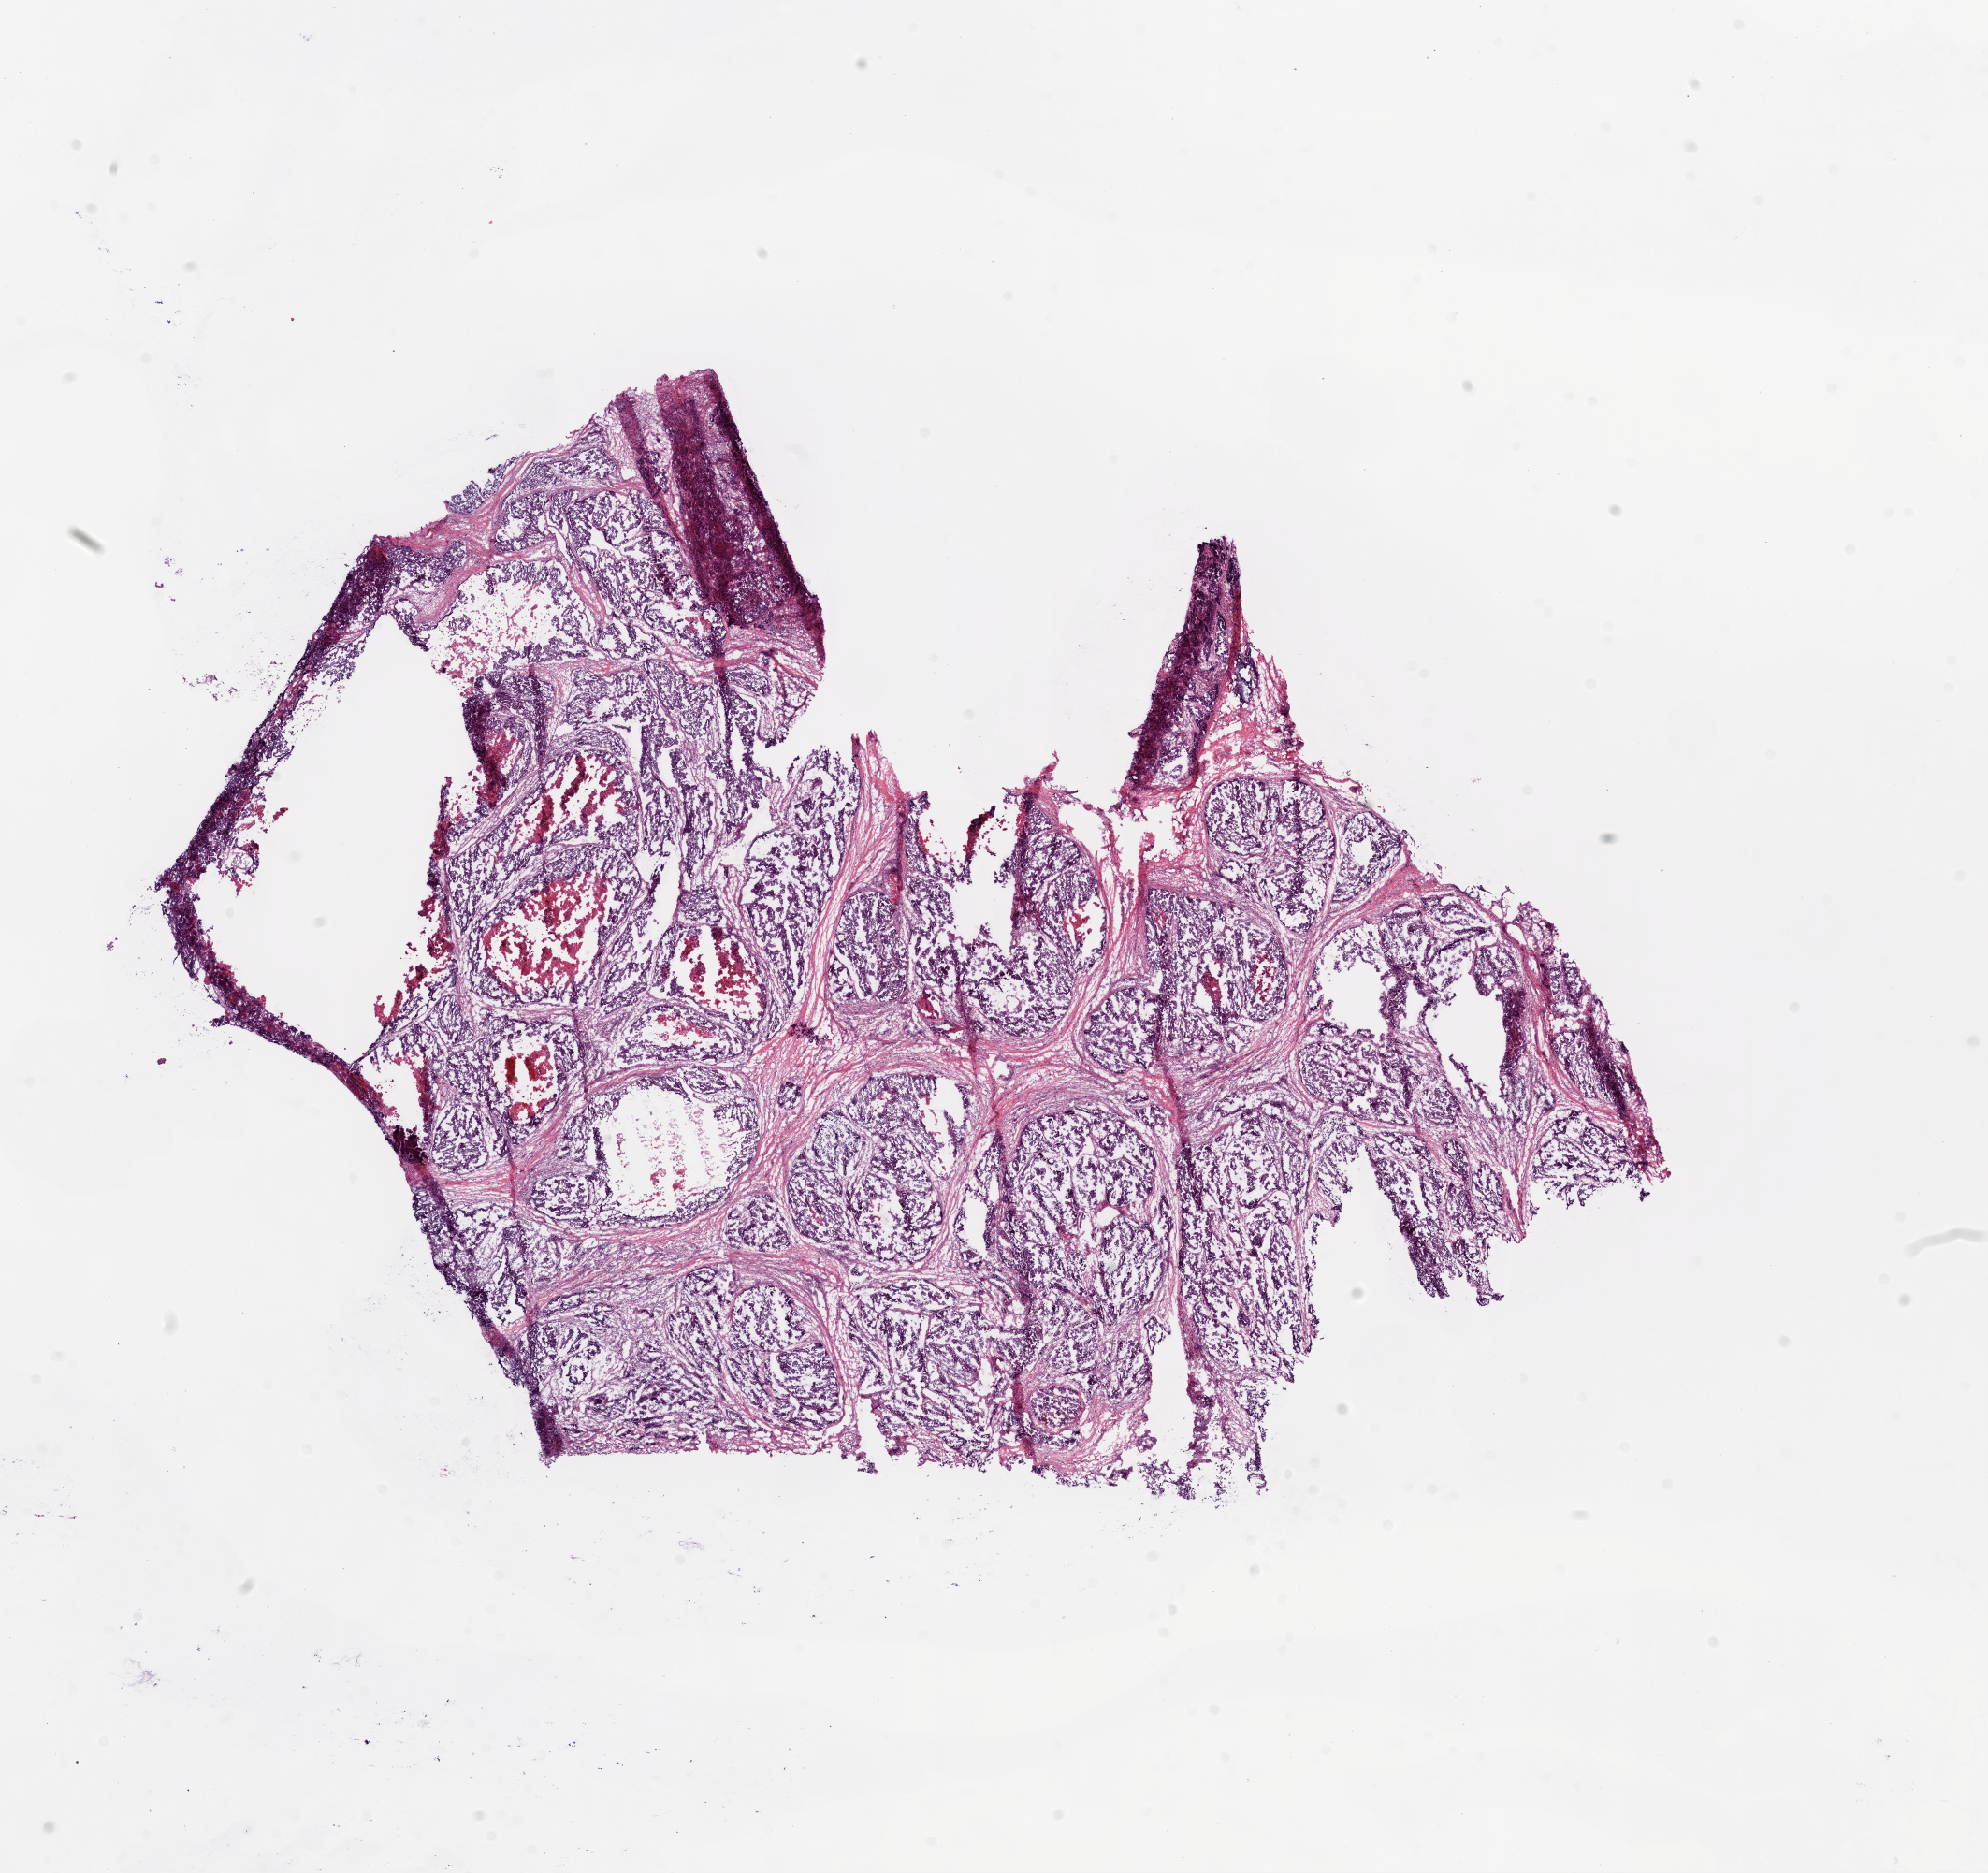
H&E whole-slide image — low-resolution overview of the scanned area, about 17.1 x 16.1 mm, frozen section from the top of the tissue portion, sample: primary tumour, ovary. Female patient; age at initial diagnosis 74 years. Histologic grade: G3 (poorly differentiated). Pathologist review of this section (percent, as recorded): tumour cells 80%, tumour nuclei 90%, normal cells 0%, stromal cells 10%, necrosis 10%.
Histologic diagnosis: Serous cystadenocarcinoma, NOS. Laterality: bilateral. FIGO stage: IIIB.